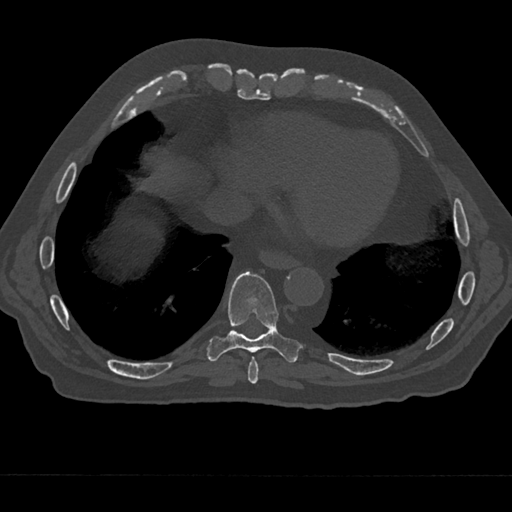
CT including the spine, one axial slice. Position 265 of 797 along the scan axis. Reconstruction kernel Br40s/3. 120 kVp. Bone window (W 1800 / L 400 HU). 0.5 mm slice thickness. 512 × 512 image matrix, field of view 377 × 377 mm. Patient: male, 75 years. Case-level facts recorded for this patient, not image findings: primary cancer: renal.
Annotated regions visible in this slice (semi-automatic segmentation, software-assisted and operator-edited):
- T8 vertebra: box from (x=248, y=356) to (x=259, y=384) px
- T9 vertebra: (x=207, y=271)–(x=302, y=363)